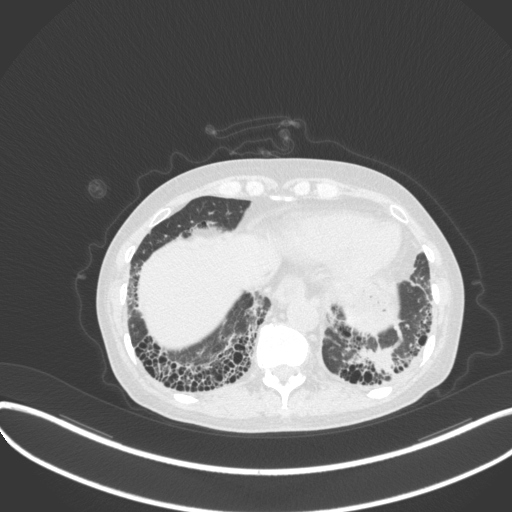
Chest CT, one axial slice. Position 62 of 373 along the scan axis. Reconstruction kernel B31f. 120 kVp. Lung window (W 1500 / L -600 HU). 512 × 512 image matrix, field of view 400 × 400 mm. Female patient, age 56 years. From the clinical record (not read from this slice): clinical TNM (as recorded): T1 N0 M0.
Annotated regions visible in this slice (rectangle marked by the reading radiologist):
- lung tumour (recorded histology: adenocarcinoma): bounding box [x1, y1, x2, y2] px = [345, 346, 401, 378]